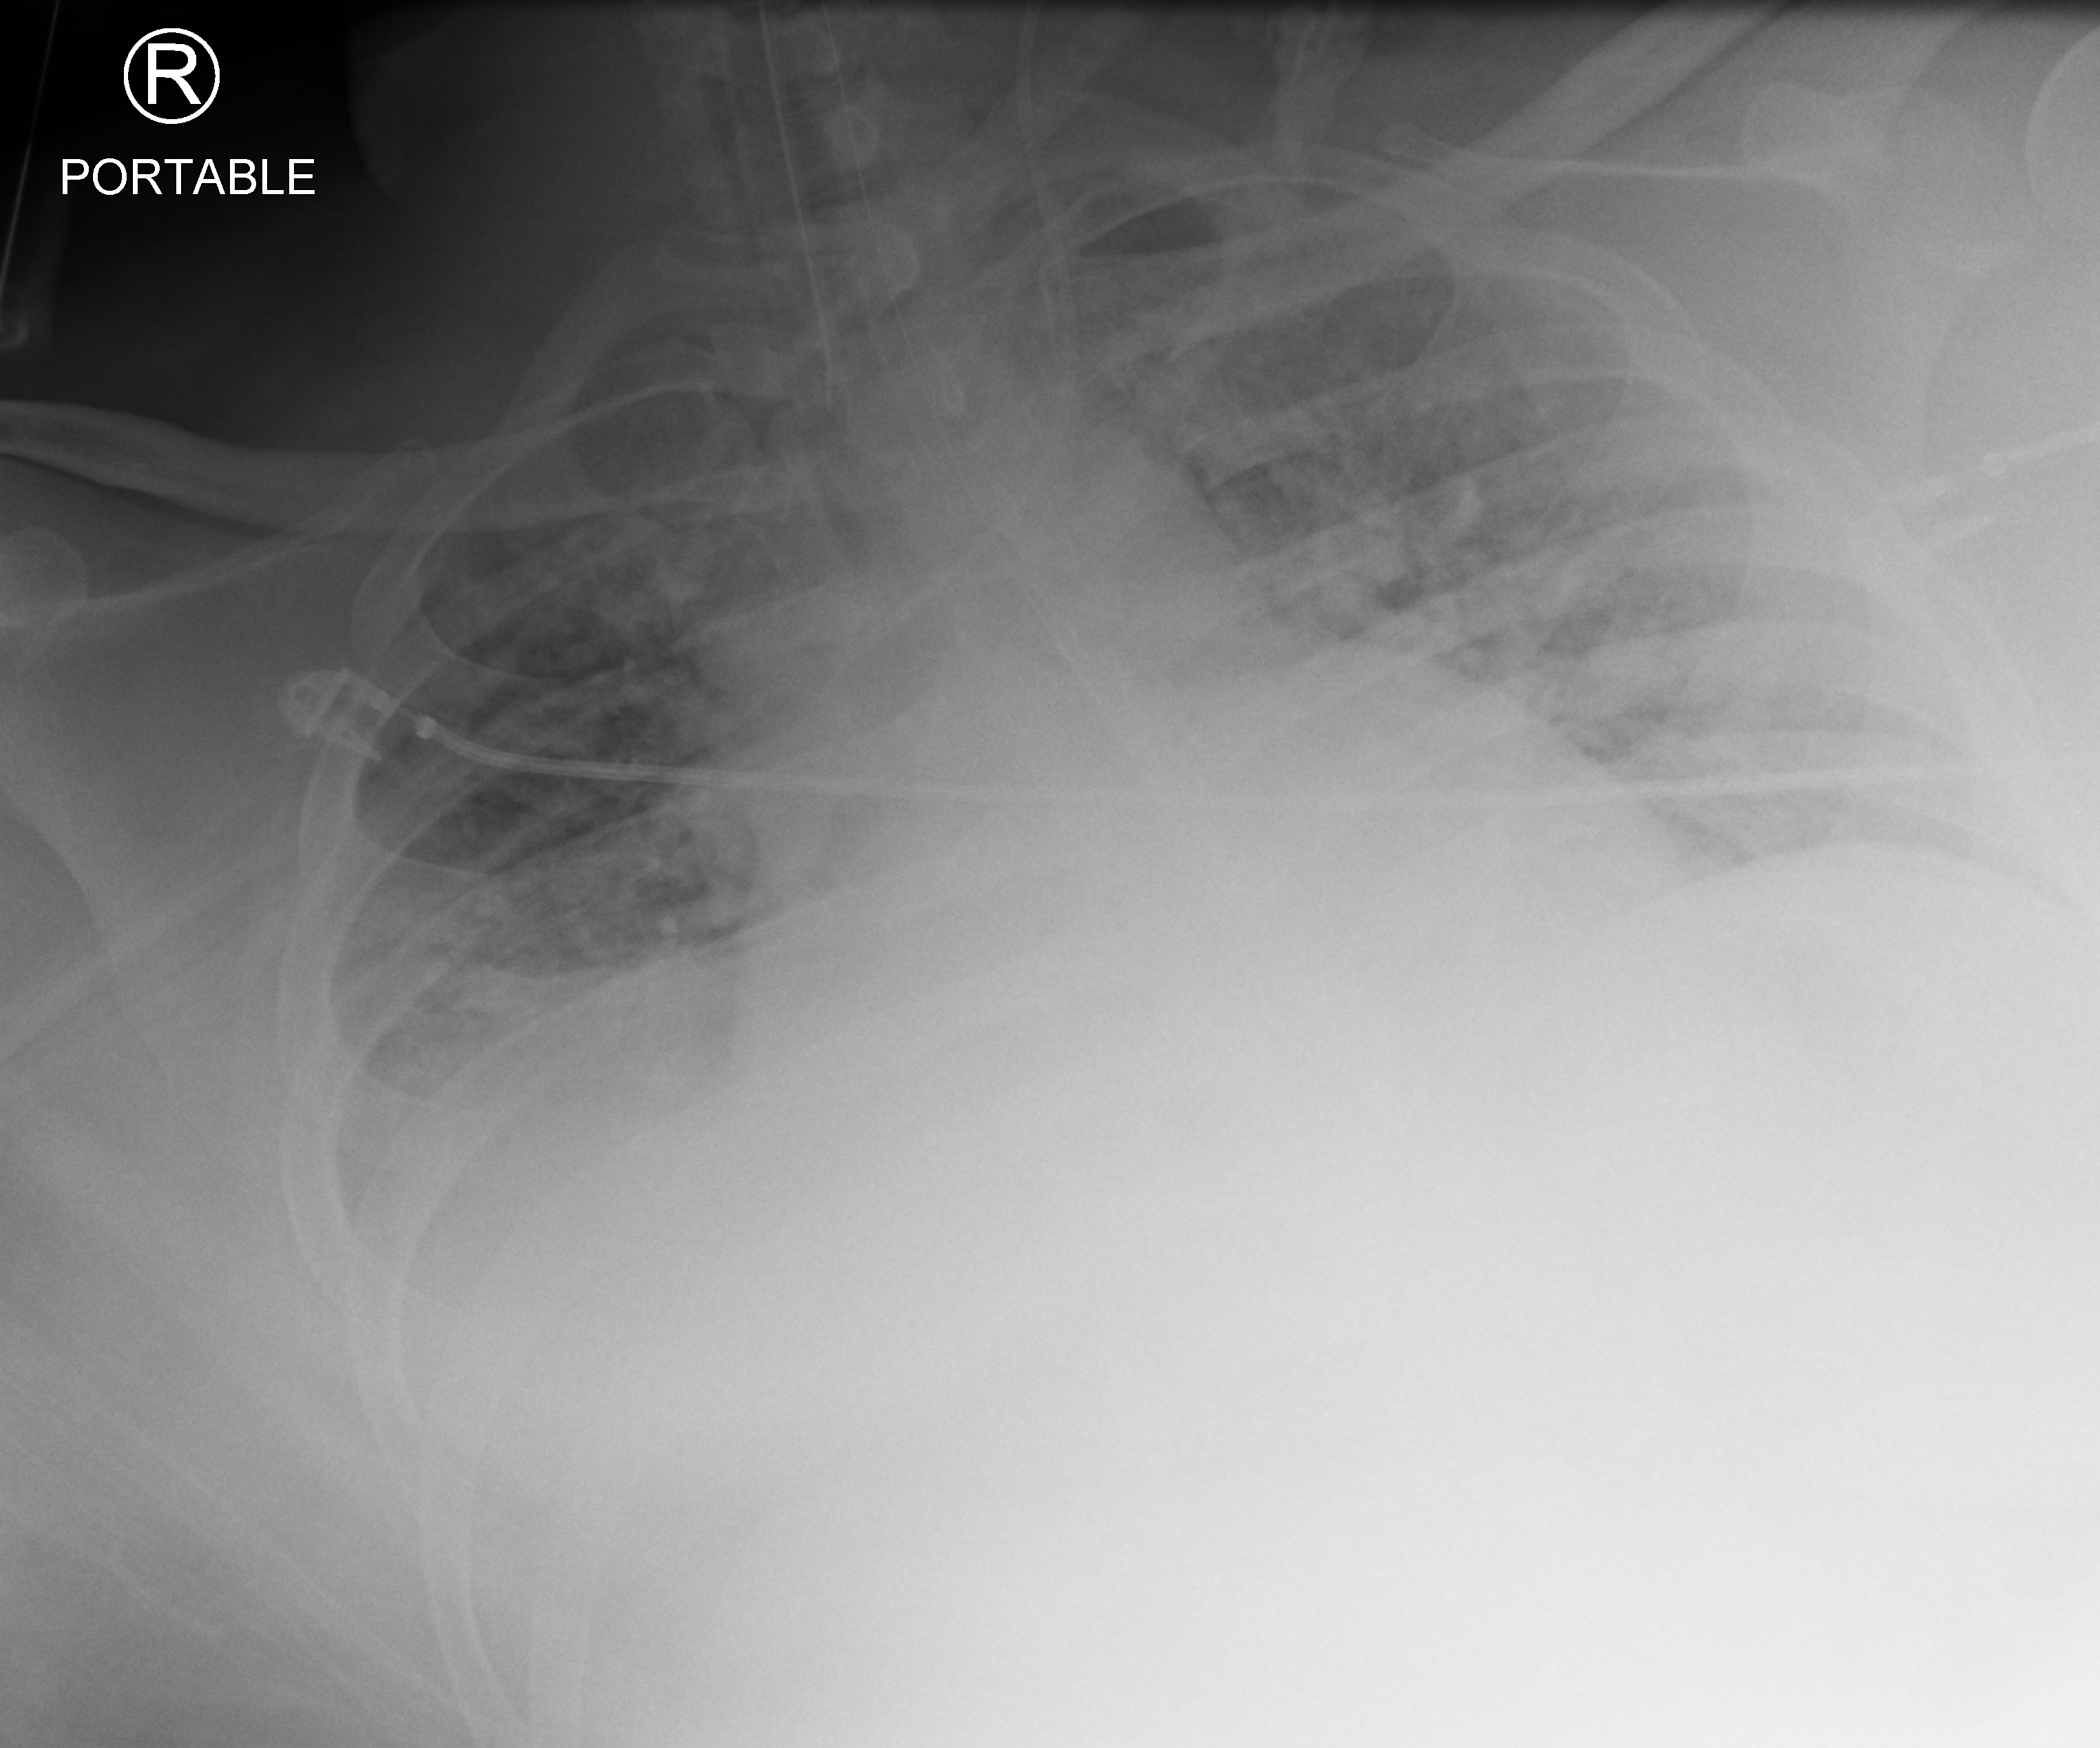
Portable chest radiograph, anteroposterior (AP) projection. Patient hospitalised with COVID-19; male, aged 18–59 years.
From the hospital-stay record, not from the radiograph (when in the stay this image was taken is not recorded): length of hospital stay: 69 days; chronic kidney disease (admission record): no; hypertension (admission record): no.